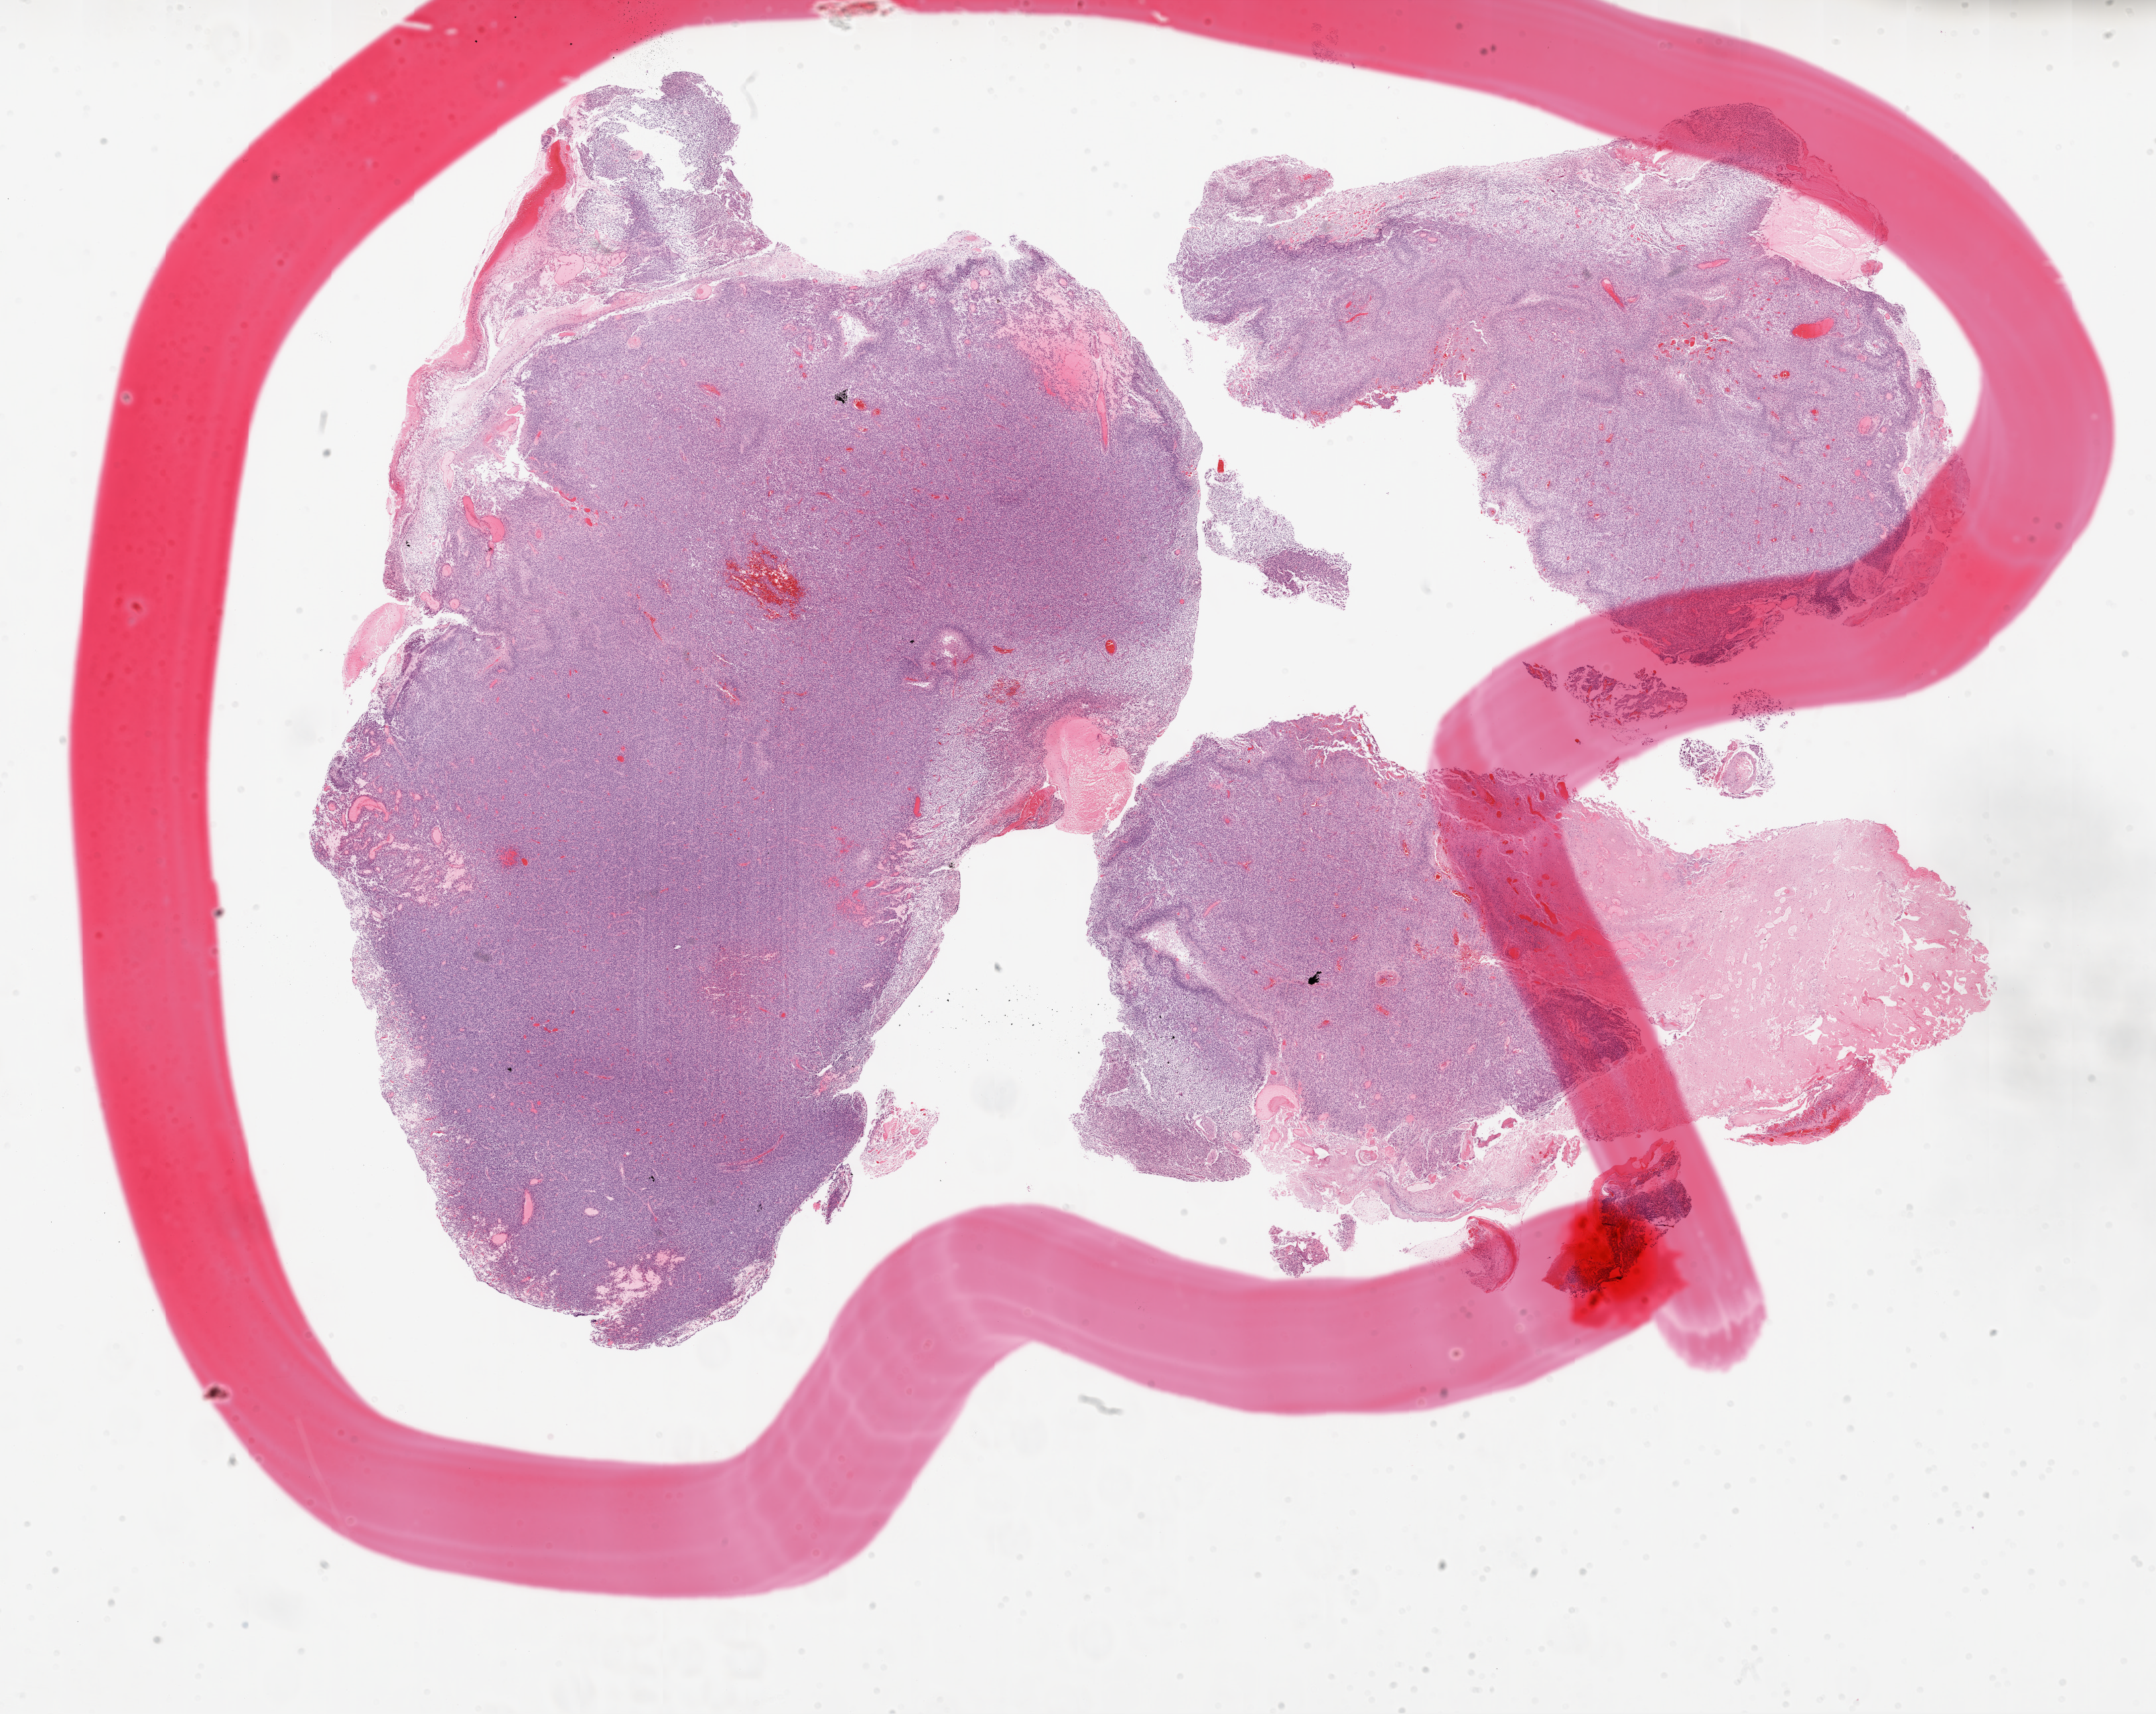
Whole-slide histology image, H&E-stained, low-resolution overview of the scanned area, about 26.1 x 20.7 mm. Formalin-fixed paraffin-embedded (FFPE) diagnostic section. Brain, primary tumour sample. Patient: male, age at initial diagnosis 50 years.
Histologic diagnosis: Glioblastoma.